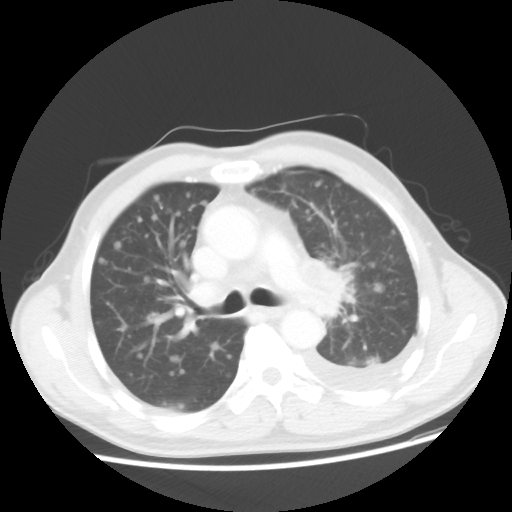
Chest CT, one axial slice; position 30 of 48 along the scan axis; 100 kVp; lung window (W 1500 / L -600 HU); 512 × 512 image matrix, field of view 362 × 362 mm. Patient: male, 55 years. Case-level facts recorded for this patient, not image findings: clinical TNM (as recorded): T2 N3 M1a; histopathological grade: G3.
Annotated regions visible in this slice (rectangle marked by the reading radiologist):
- lung tumour (recorded histology: squamous cell carcinoma): bounding box [x1, y1, x2, y2] px = [299, 250, 357, 321]